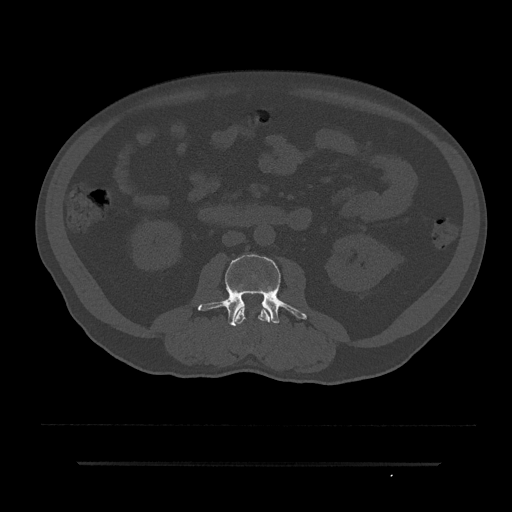
CT including the spine, one axial slice. Slice 23 of 797 in the series (ordered by position). Reconstruction kernel Br40s/3. 120 kVp. Bone window (W 1800 / L 400 HU). 512 × 512 image matrix. Male patient, age 59 years. From the clinical record (not read from this slice): primary cancer: bile ducts.
Outlined on this slice (semi-automatic segmentation, software-assisted and operator-edited):
- L2 vertebra: bounding box <234,303,271,325> (left, top, right, bottom; pixels)
- L3 vertebra: <198,254,307,326>